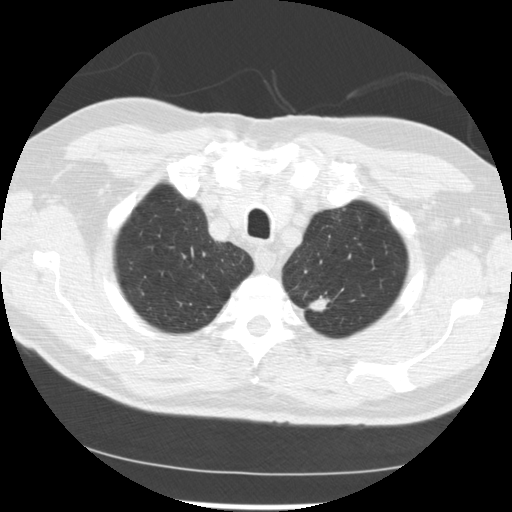
Low-dose screening chest CT, one axial slice; slice 215 of 249 in the series (ordered by position); reconstruction kernel STANDARD; lung window (W 1500 / L -600 HU); 2.5 mm slice thickness; 512 × 512 image matrix, field of view 341 × 341 mm.
Structures marked on this image (expert manual segmentation):
- lesion 2 (tumor, upper lobe of left lung): bounding box (x1, y1, x2, y2) in pixels: (309, 297, 328, 311)